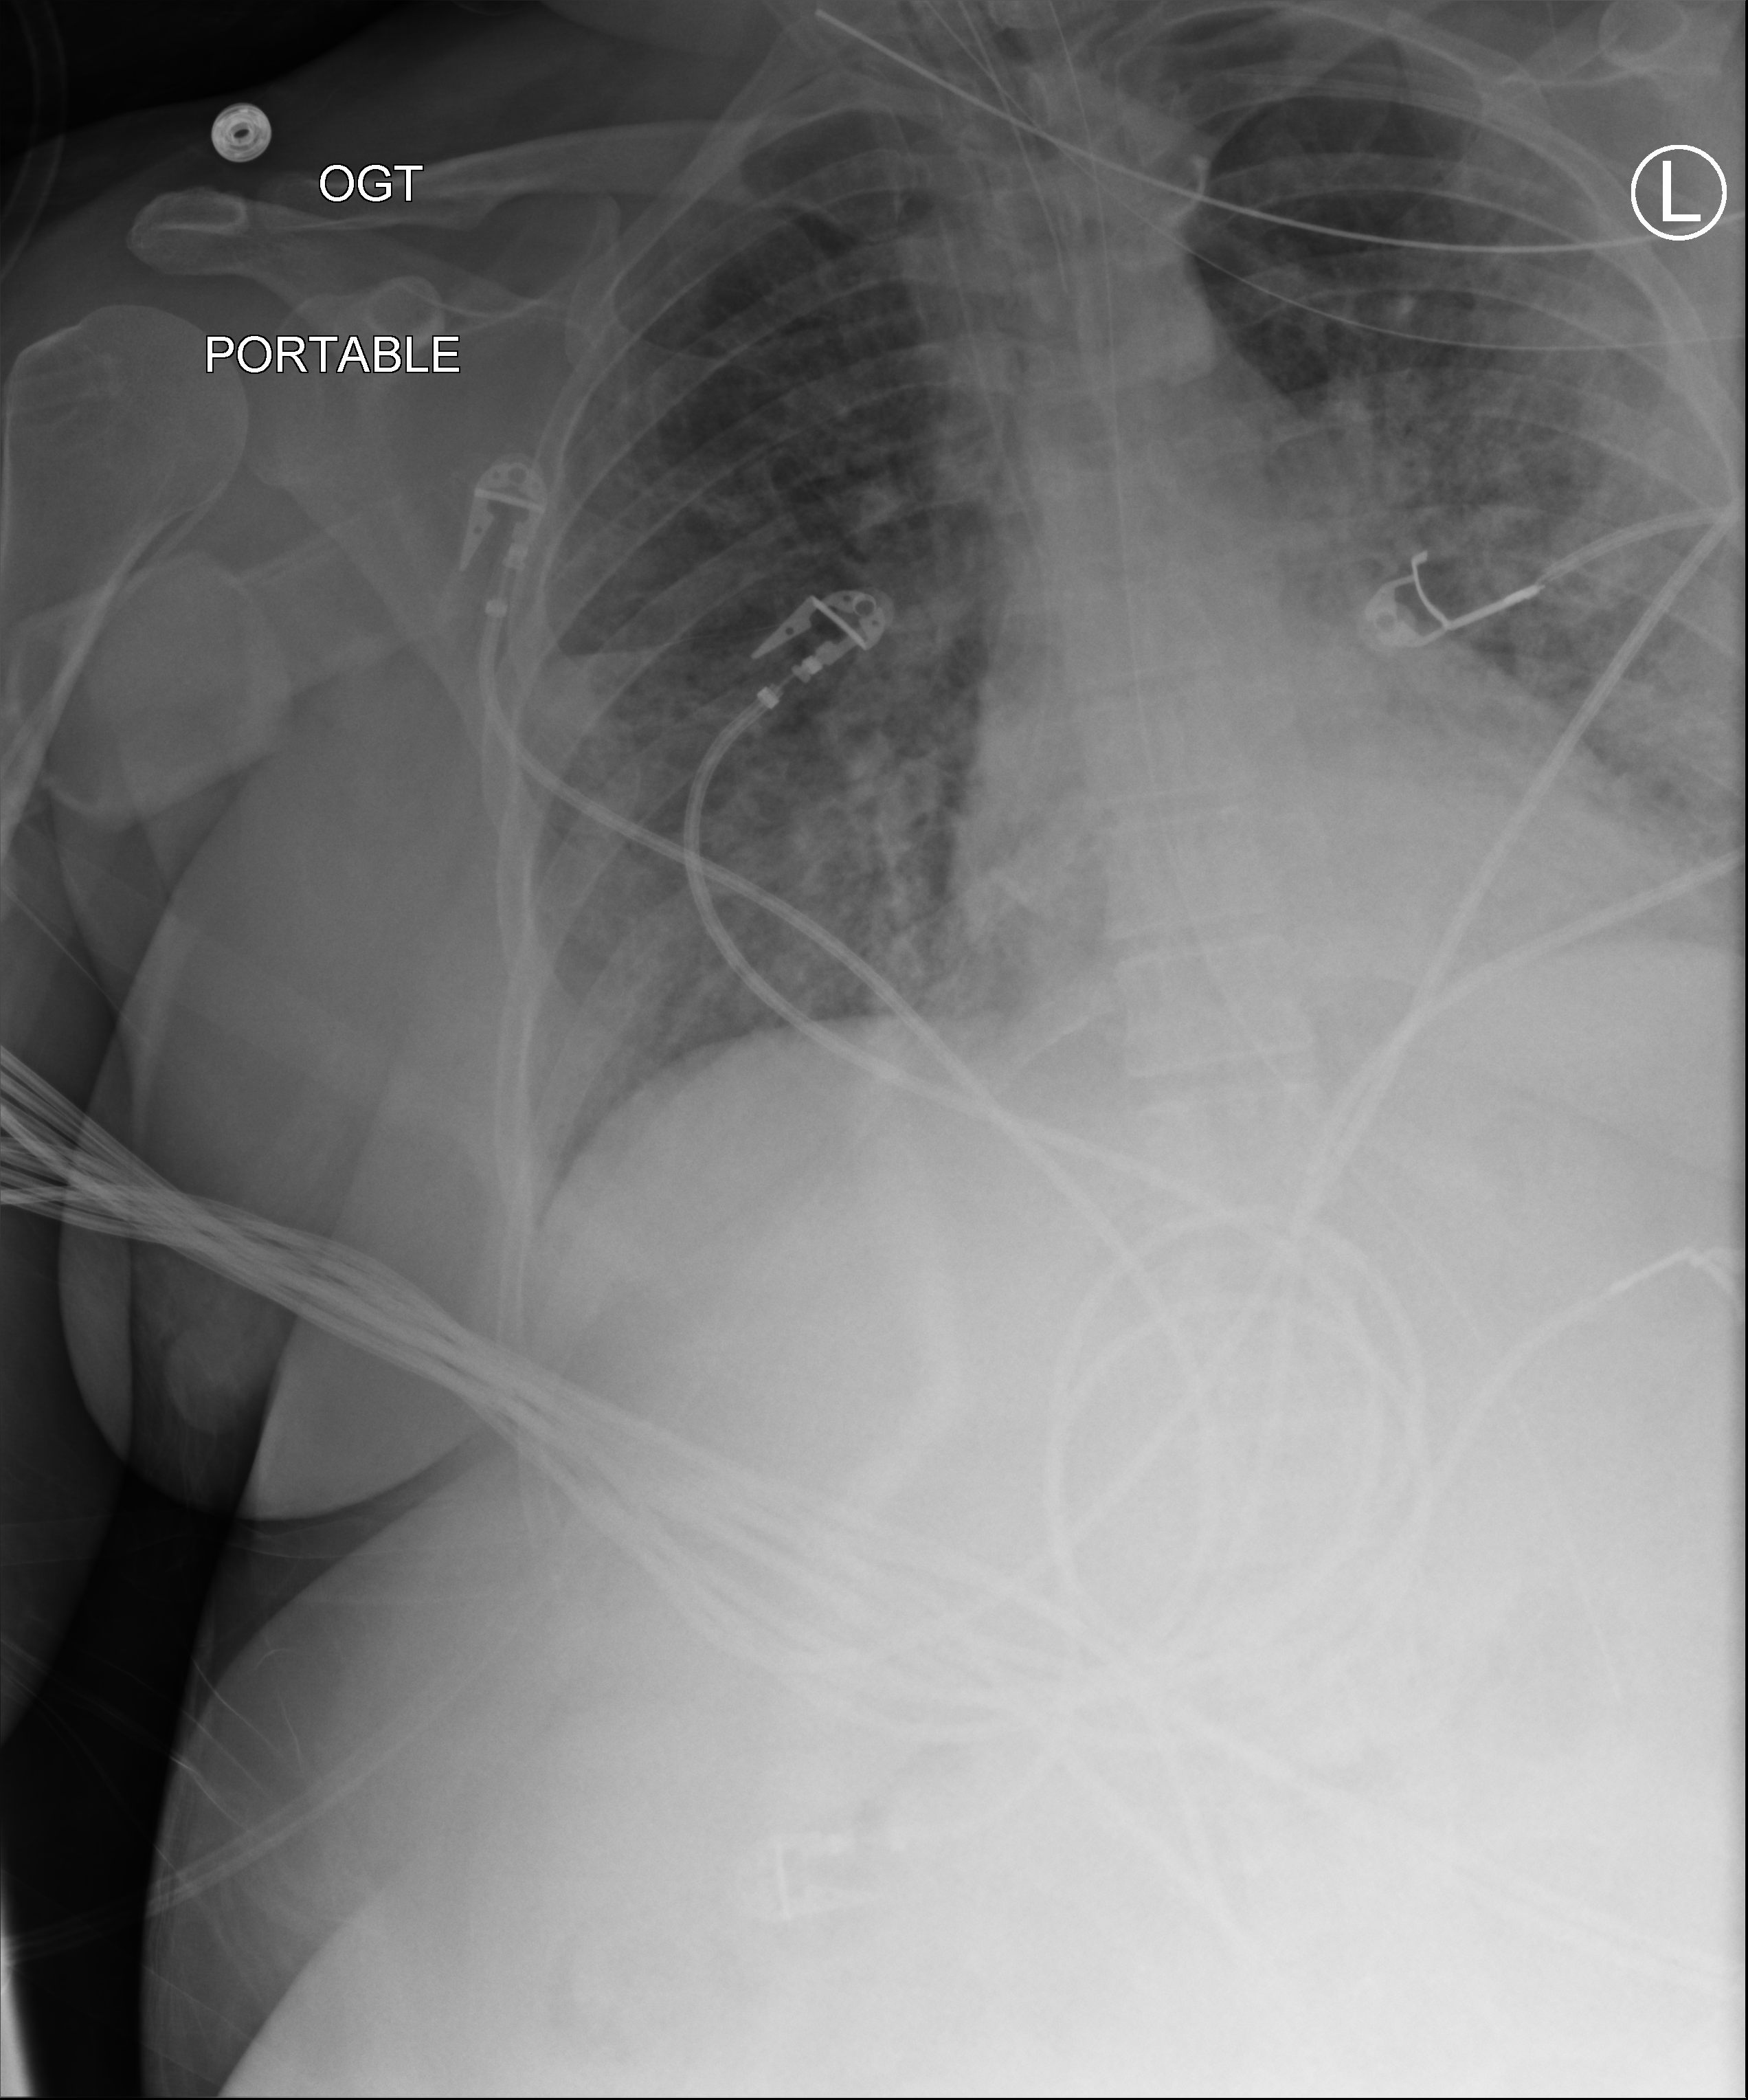
Chest X-ray (portable); anteroposterior (AP) projection. Female patient hospitalised with COVID-19, age 18–59 years.
Hospital-stay facts (about this admission, not read from this image; timing relative to this image not recorded):
- COPD (admission record): no
- other chronic lung disease (admission record): no